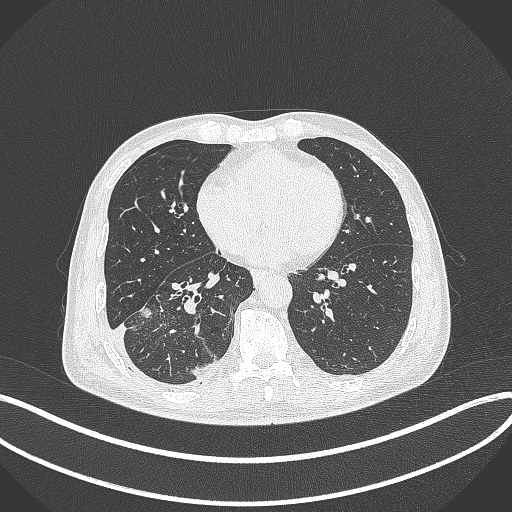
Chest CT, one axial slice. Position 150 of 388 along the scan axis. Reconstruction kernel B70f. 120 kVp. Lung window (W 1500 / L -600 HU). 1 mm slice thickness. 512 × 512 image matrix, field of view 400 × 400 mm. Male patient, age 64 years. Case-level facts recorded for this patient, not image findings: clinical TNM (as recorded): T3 N0 M0; histopathological grade: G2-3.
Annotated regions visible in this slice (rectangle marked by the reading radiologist):
- lung tumour (recorded histology: adenocarcinoma): bounding box (x1, y1, x2, y2) in pixels: (138, 302, 155, 320)